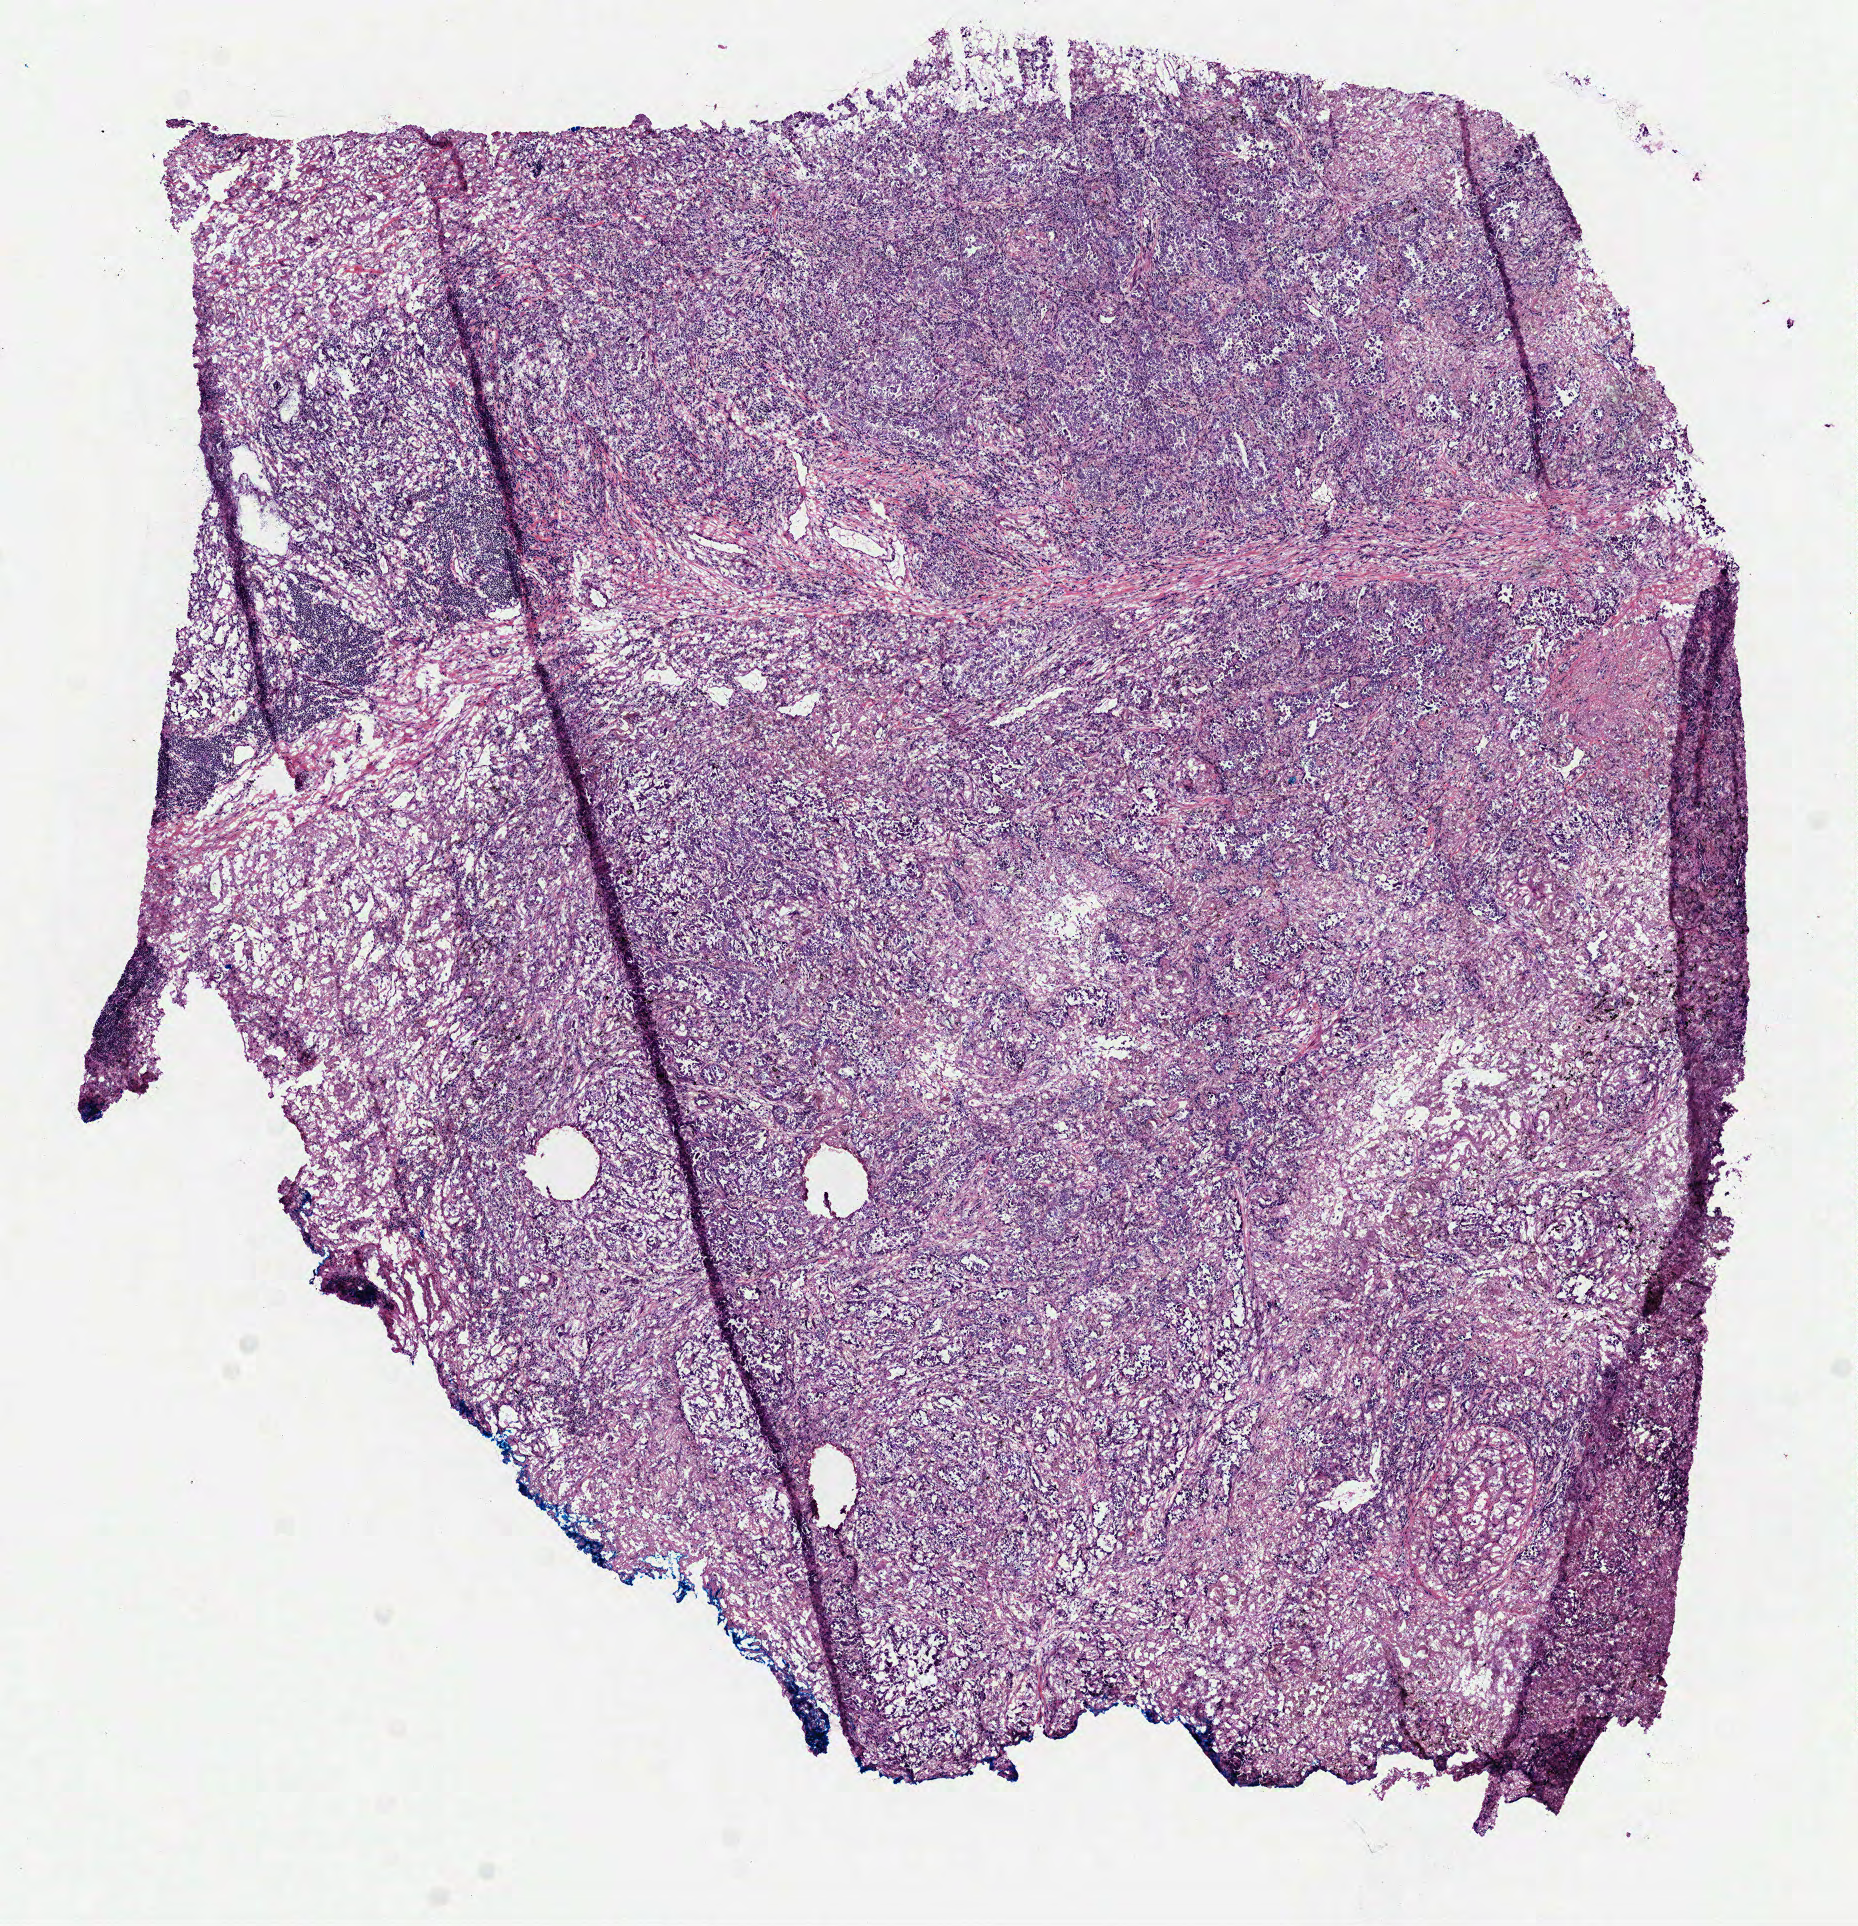
Whole-slide histology image, Hematoxylin and eosin (H&E) stained, low-resolution overview of the scanned area, about 7.5 x 7.8 mm (from a 40x scan). Frozen section from the top of the tissue portion. Lung, primary tumour sample. Female patient; age at initial diagnosis 64 years.
Histologic diagnosis: Adenocarcinoma, NOS (upper lobe, lung).